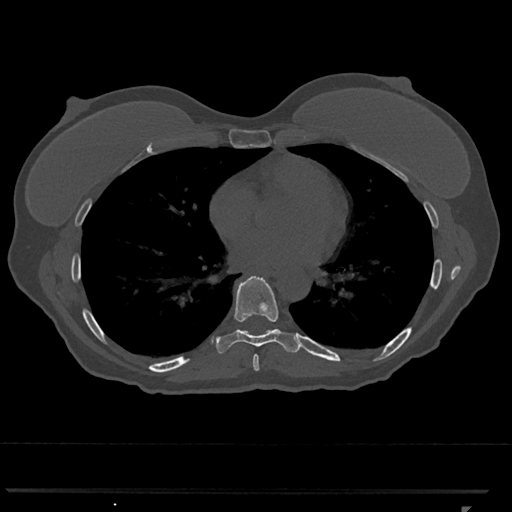
CT including the spine, one axial slice. Slice 667 of 793 in the series (ordered by position). Reconstruction kernel Br40s/3. Bone window (W 1800 / L 400 HU). 512 × 512 image matrix. Patient: female, 62 years. Case-level facts recorded for this patient, not image findings: primary cancer: renal.
Annotated regions visible in this slice (semi-automatic segmentation, software-assisted and operator-edited):
- T7 vertebra: bounding box [x1, y1, x2, y2] px = [253, 354, 259, 371]
- T8 vertebra: [216, 275, 300, 354]